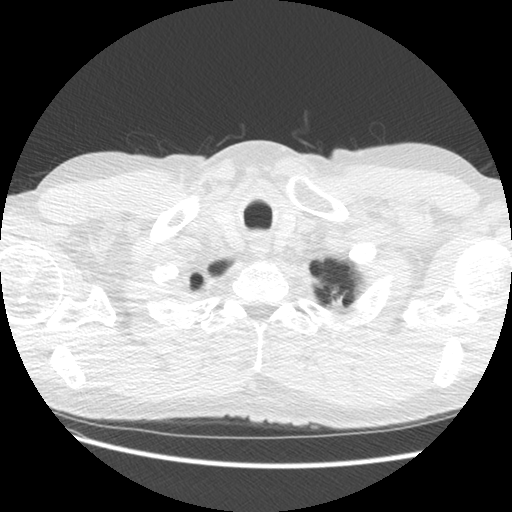
Low-dose screening chest CT, one axial slice; slice 121 of 131 in the series (ordered by position); lung window (W 1500 / L -600 HU); 2.5 mm slice thickness; 512 × 512 image matrix.
Annotated regions visible in this slice (outlined manually by an expert reader):
- lesion 1 (tumor, upper lobe of left lung): bounding box [x1, y1, x2, y2] px = [327, 292, 345, 308]